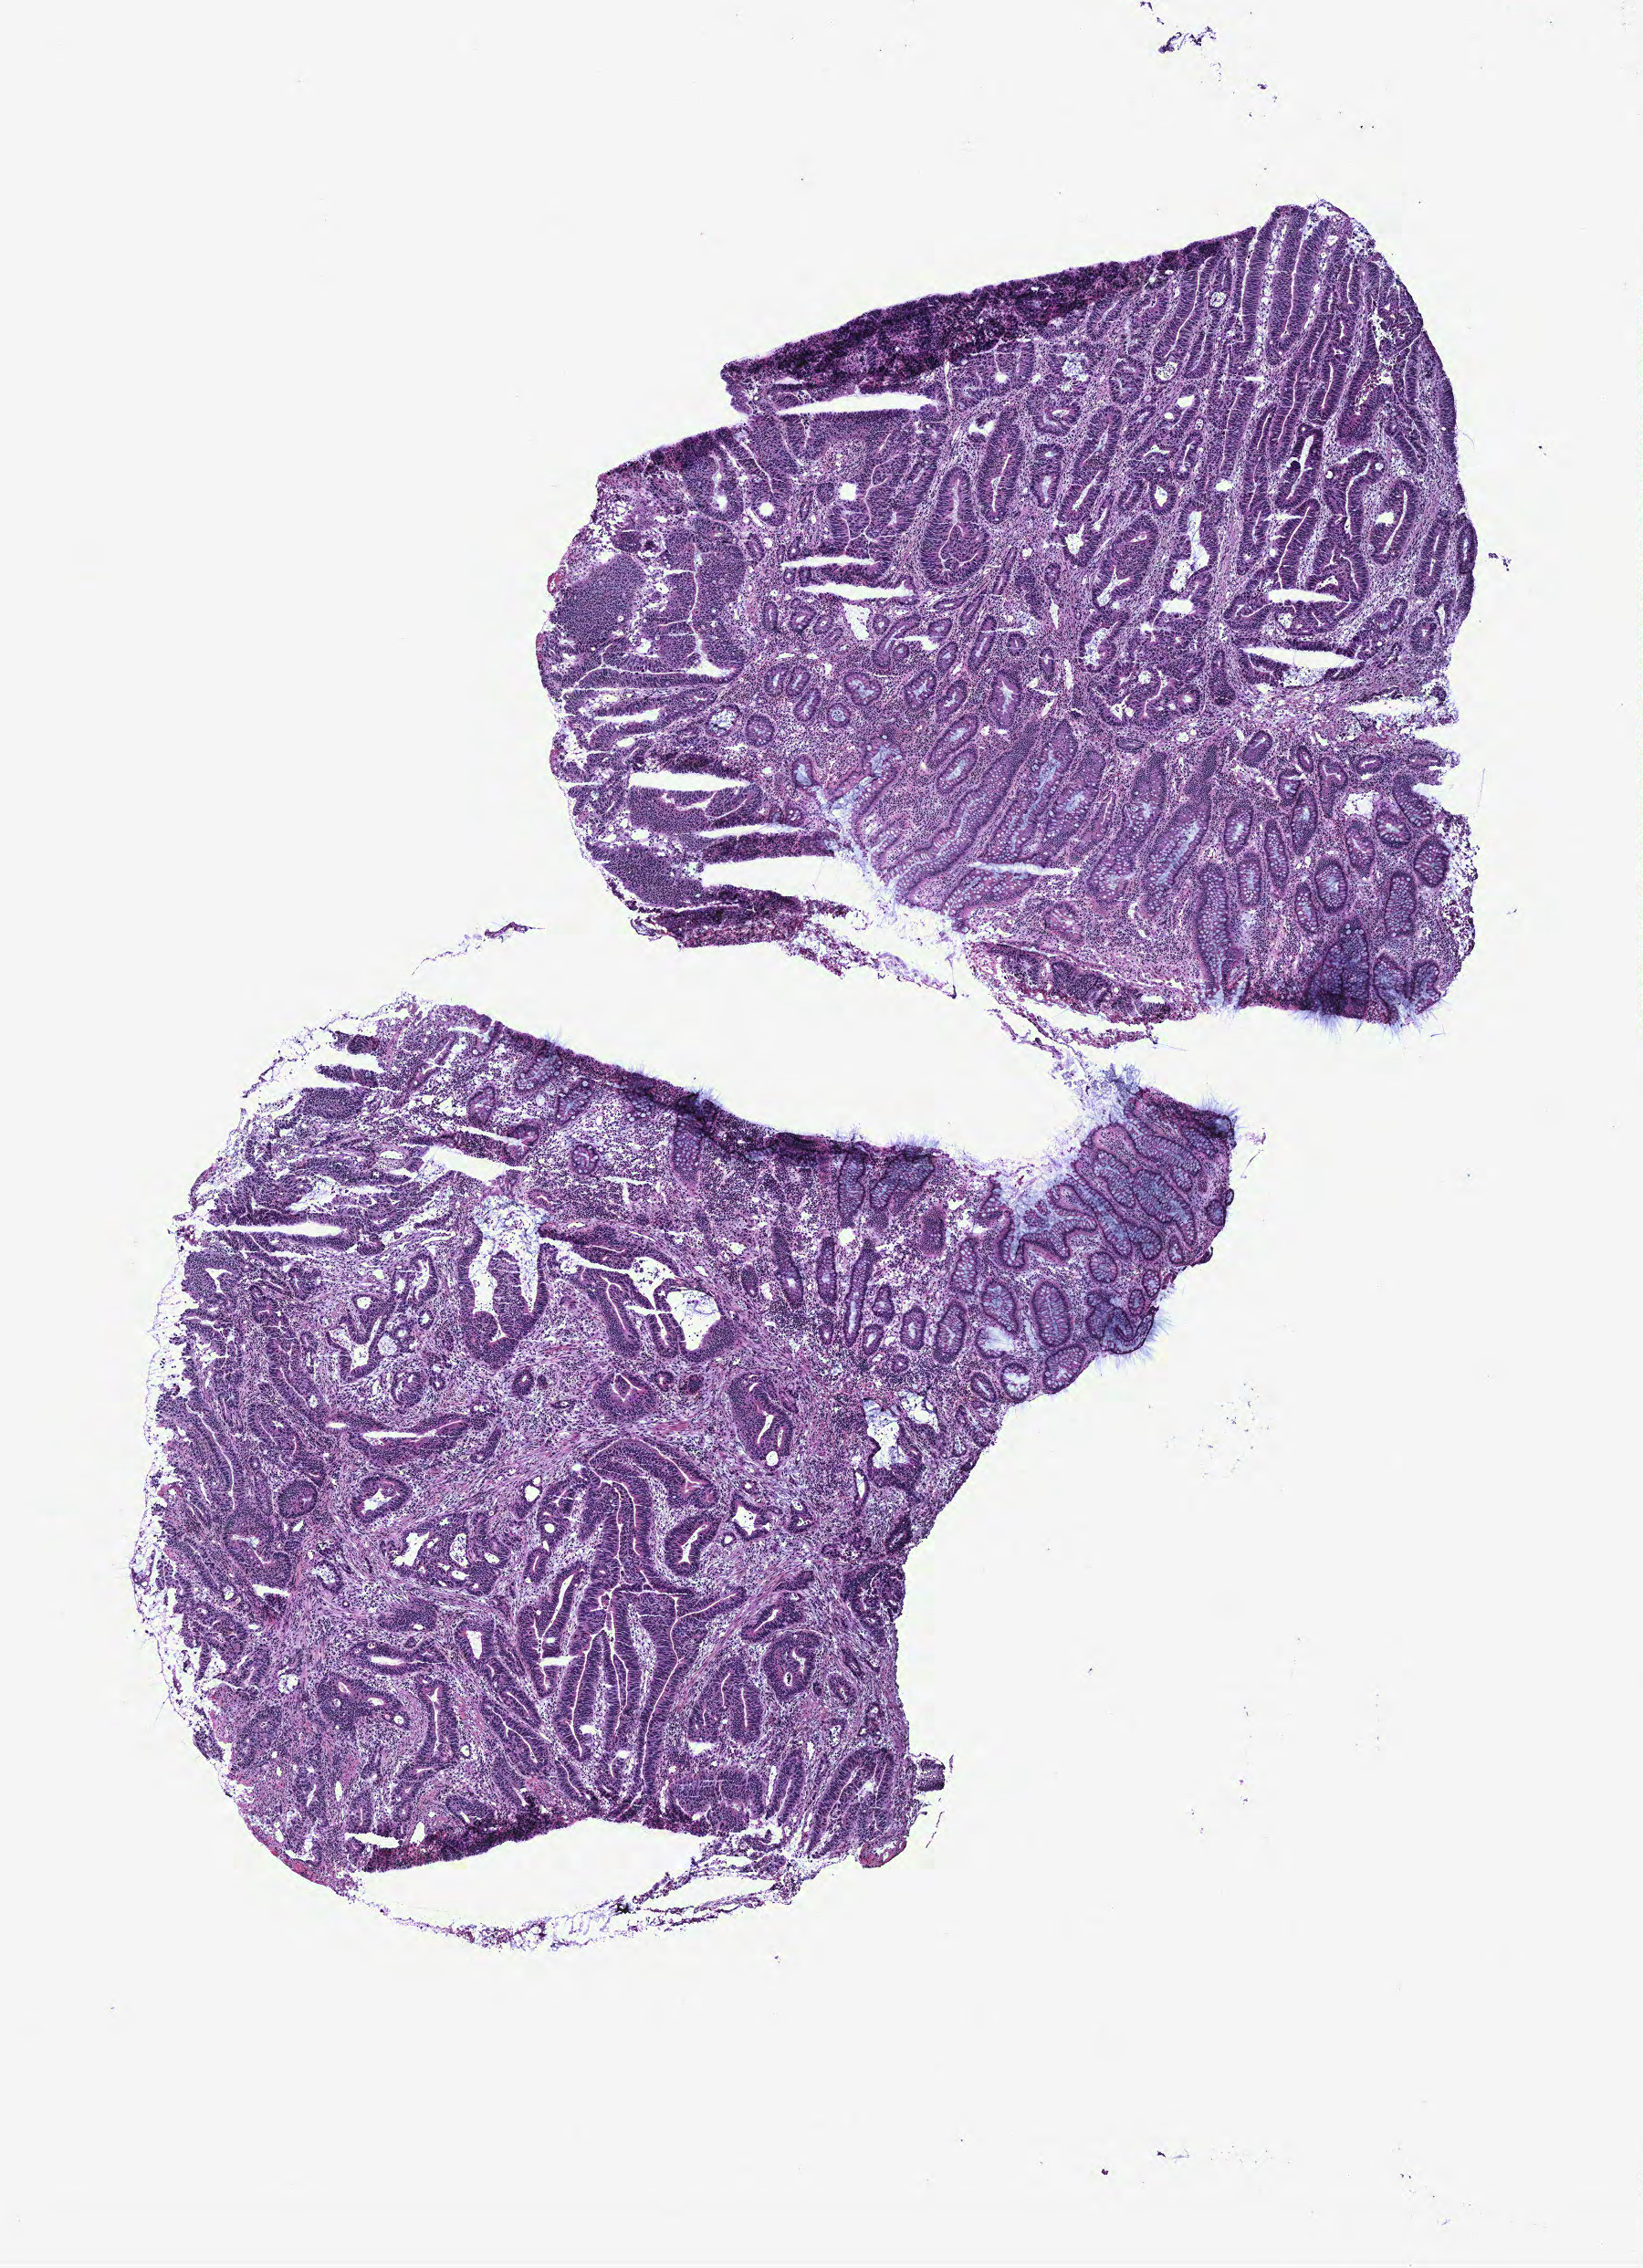
Hematoxylin and eosin (H&E) stained whole-slide image — a low-resolution overview of the entire scanned area, about 7.2 x 9.9 mm (acquisition: 40x scan), colon, normal (non-tumour) tissue. Patient: male, age 57 years.
This section: normal (non-tumour) tissue from the same patient. Patient diagnosis: Adenocarcinoma, NOS.